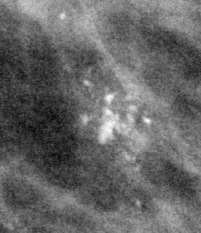
Region of interest cut from a scanned film mammogram (one marked finding), left breast, MLO view.
- Calcifications, morphology pleomorphic / fine linear branching, distribution regional; BI-RADS assessment category 5; pathology result (as recorded, not read from the image): malignant.